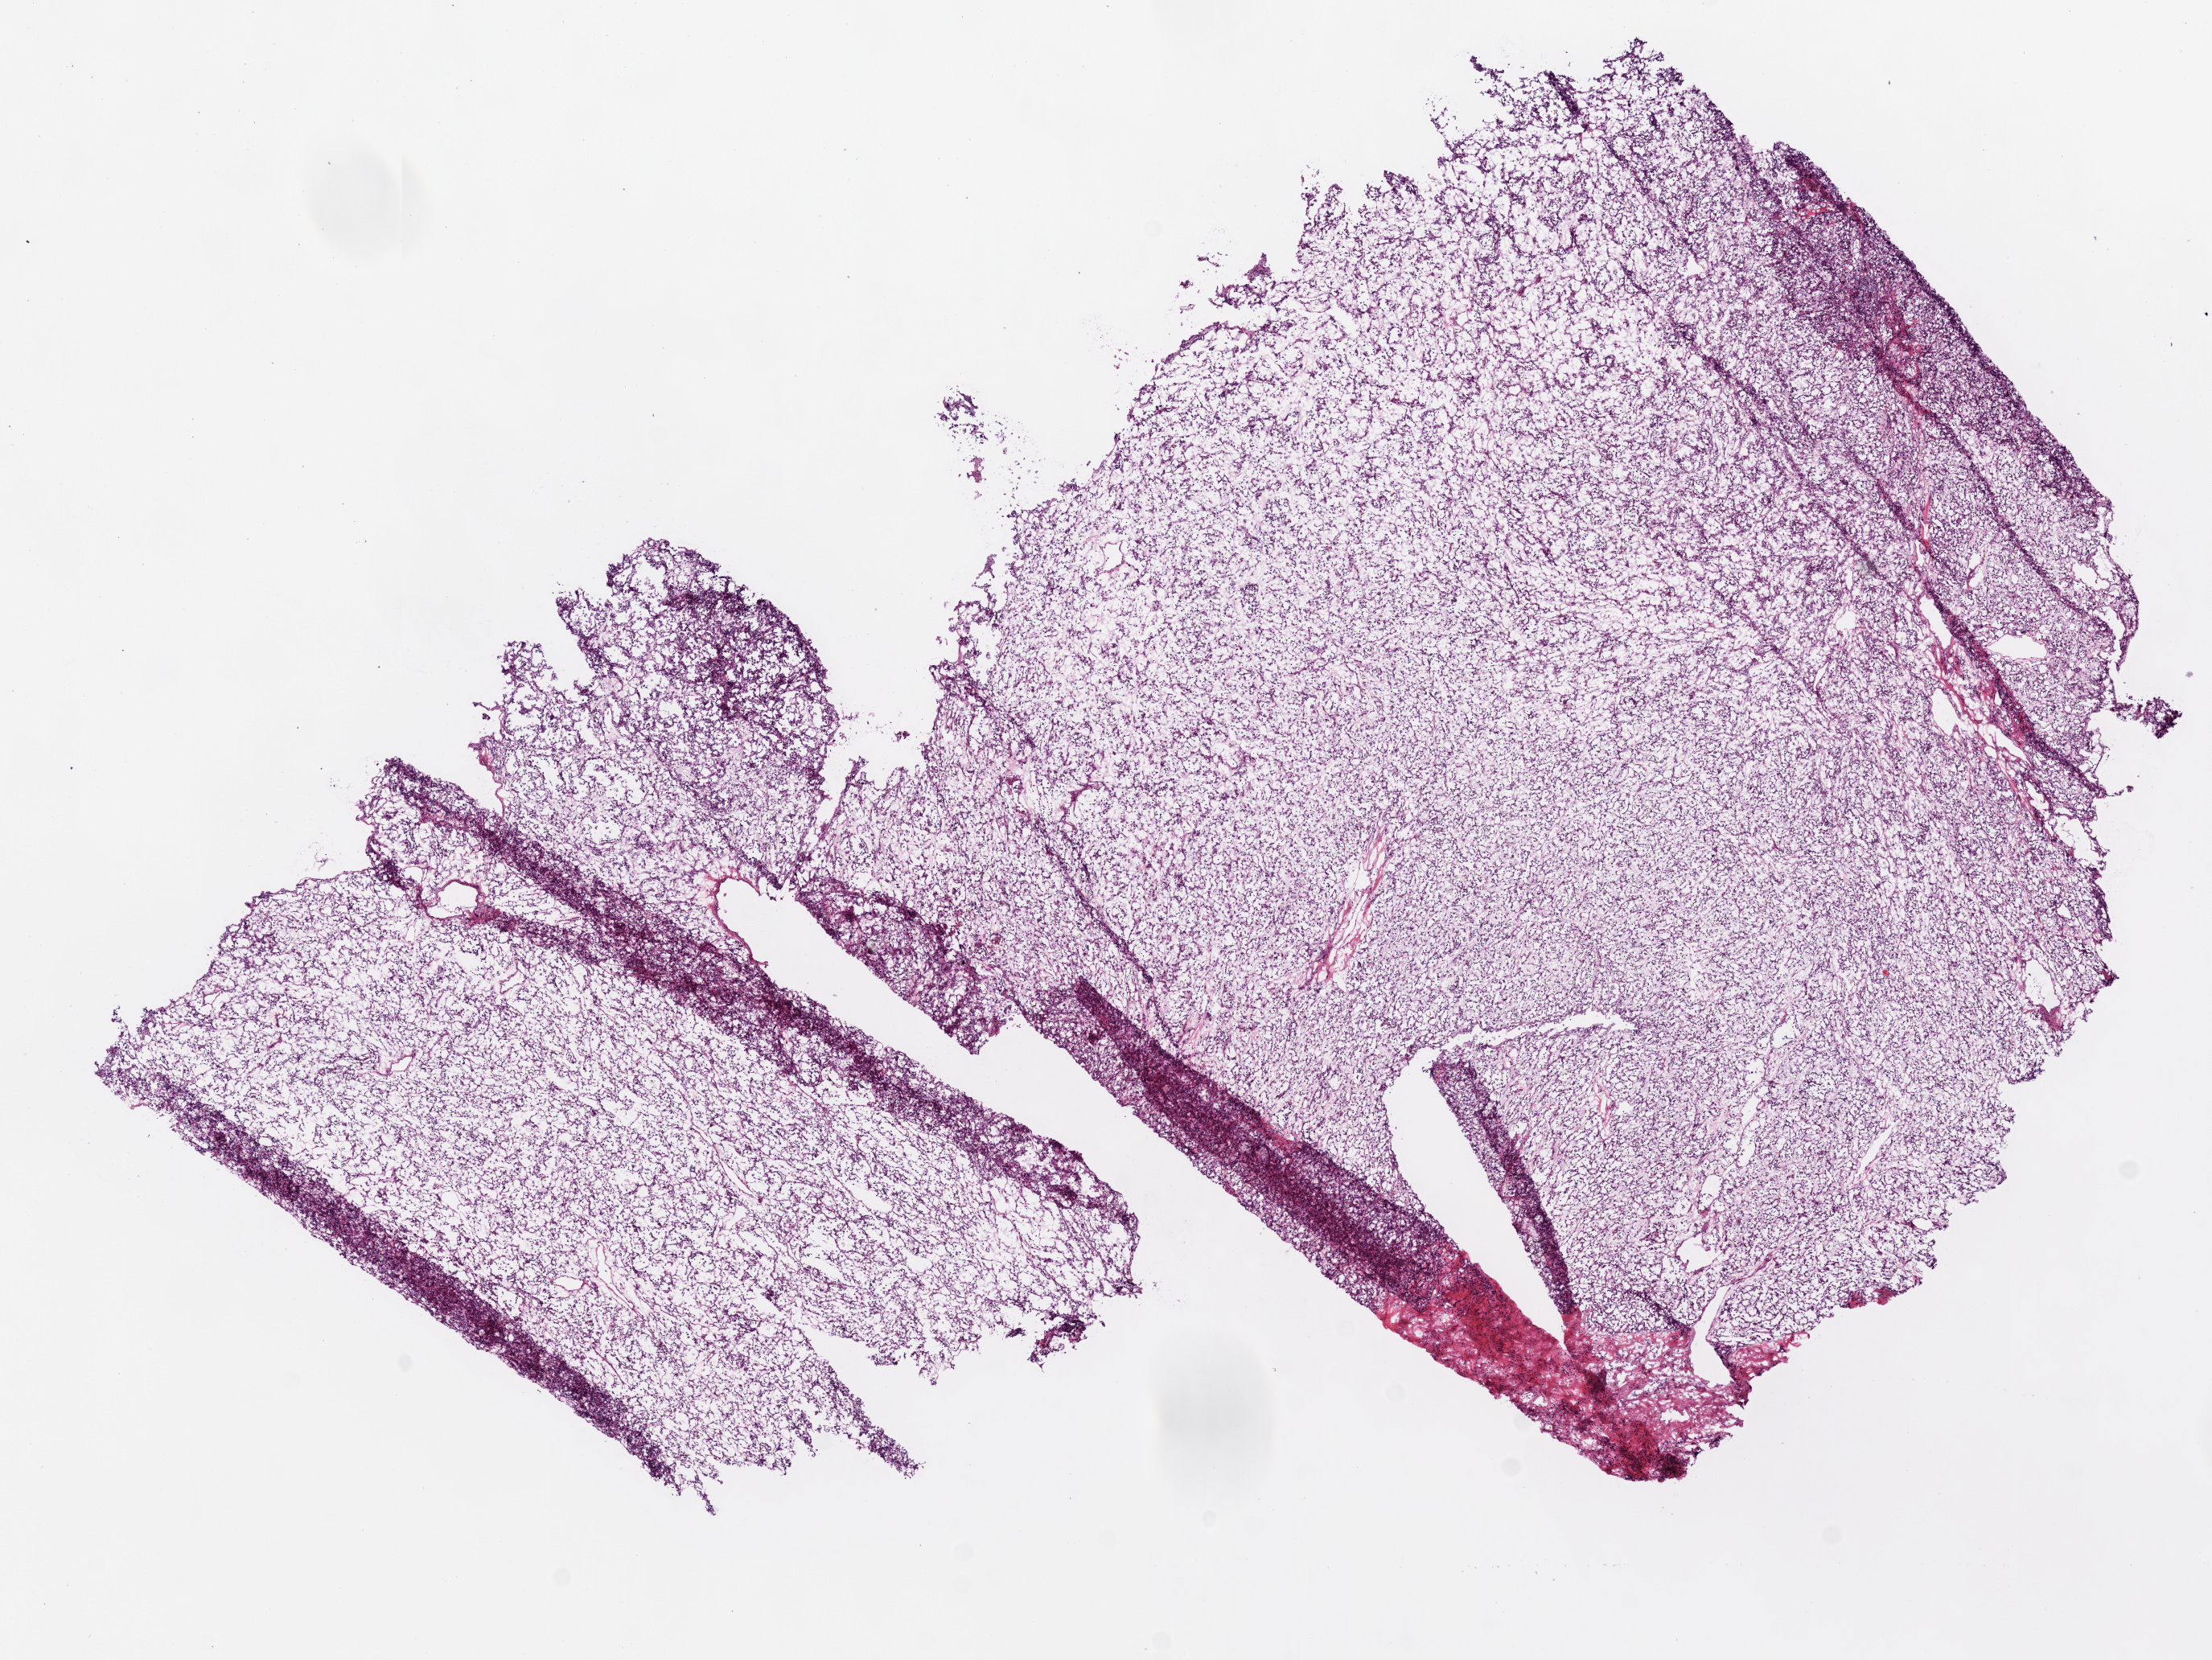
H&E whole-slide image, a low-resolution overview of the entire scanned area, about 11.0 x 8.3 mm (from a 20x scan). Frozen section from the top of the tissue portion. Sample: primary tumour, kidney. Patient: female, age at initial diagnosis 34 years. Histologic grade: G2 (moderately differentiated). Composition of this section per pathologist review: tumour cells 95%, tumour nuclei 70%, normal cells 0%, stromal cells 5%, necrosis 0%.
AJCC pathologic stage: I. Diagnosis: Clear cell adenocarcinoma, NOS.